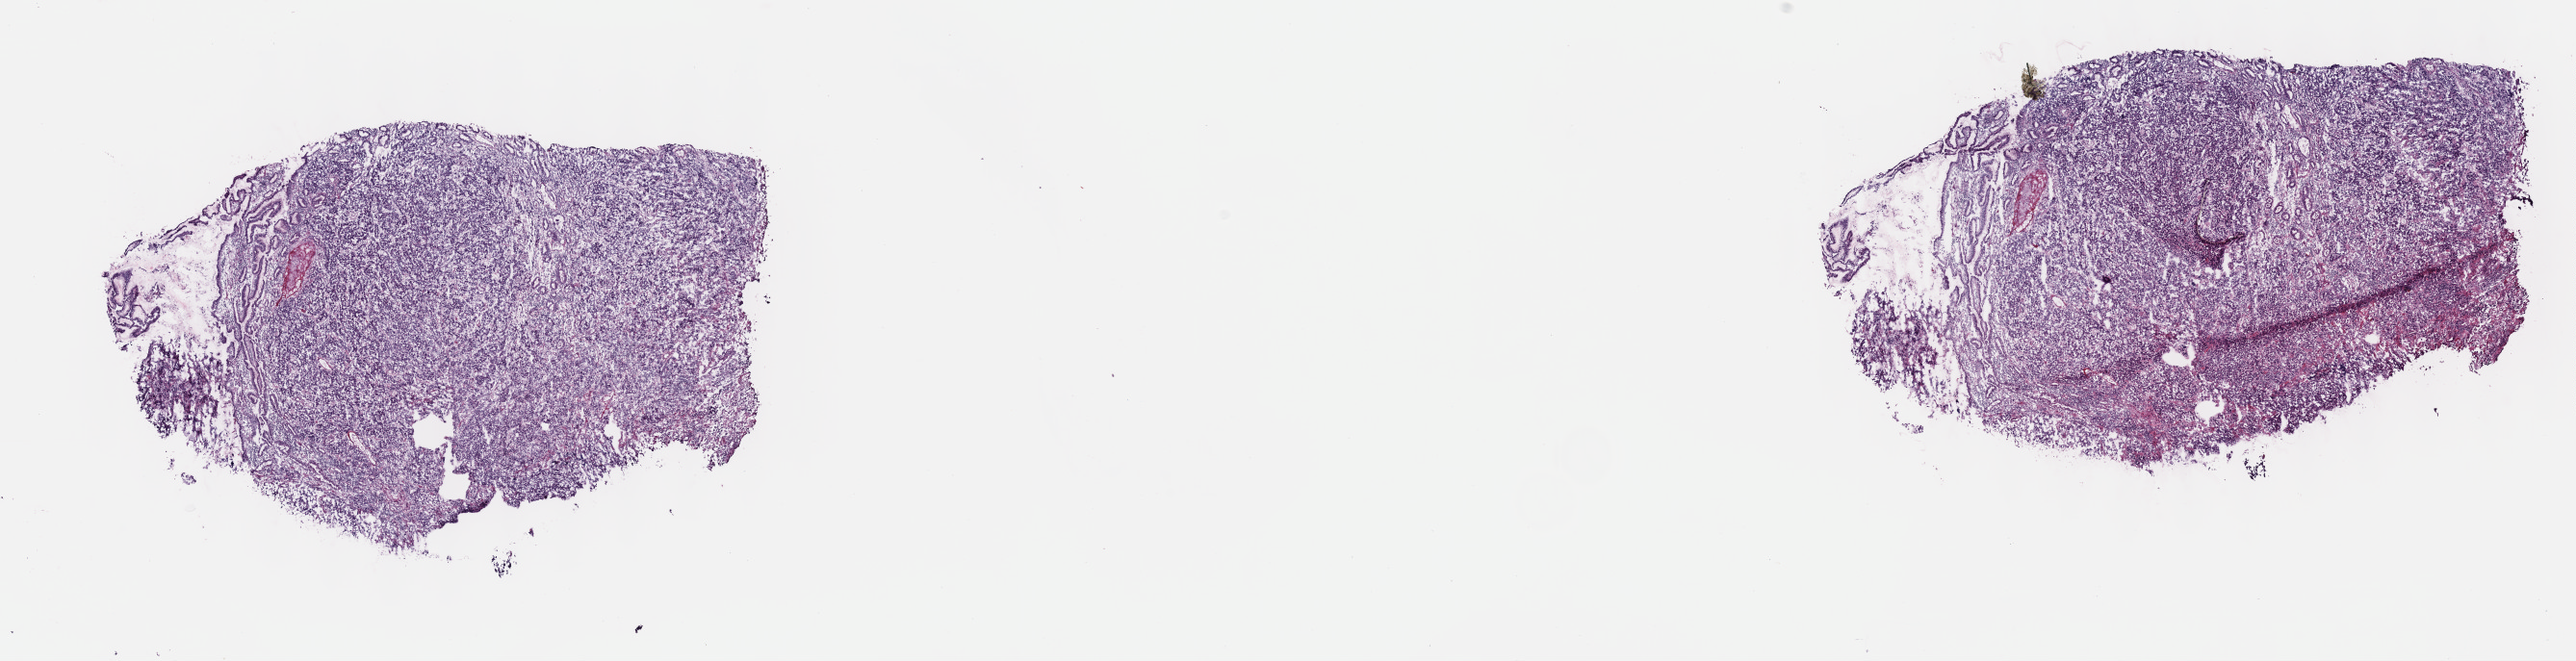
Whole-slide histology image, H&E-stained — shown as a low-resolution overview of the whole scanned area (about 21.6 x 5.6 mm, slide scanned at 40x), frozen section from the top of the tissue portion, stomach, primary tumour sample. Male patient; age at initial diagnosis 66 years. Histologic grade: G3 (poorly differentiated). Composition of this section per pathologist review: tumour cells 93%, tumour nuclei 80%, normal cells 7%, stromal cells 0%, necrosis 0%. Inflammatory infiltration, as recorded: lymphocyte infiltration 3%, monocyte infiltration 0%, neutrophil infiltration 0%.
* pathologic diagnosis: Adenocarcinoma, intestinal type (fundus of stomach)
* TNM: T3 N3 M0
* AJCC pathologic stage: IV (6th edition)